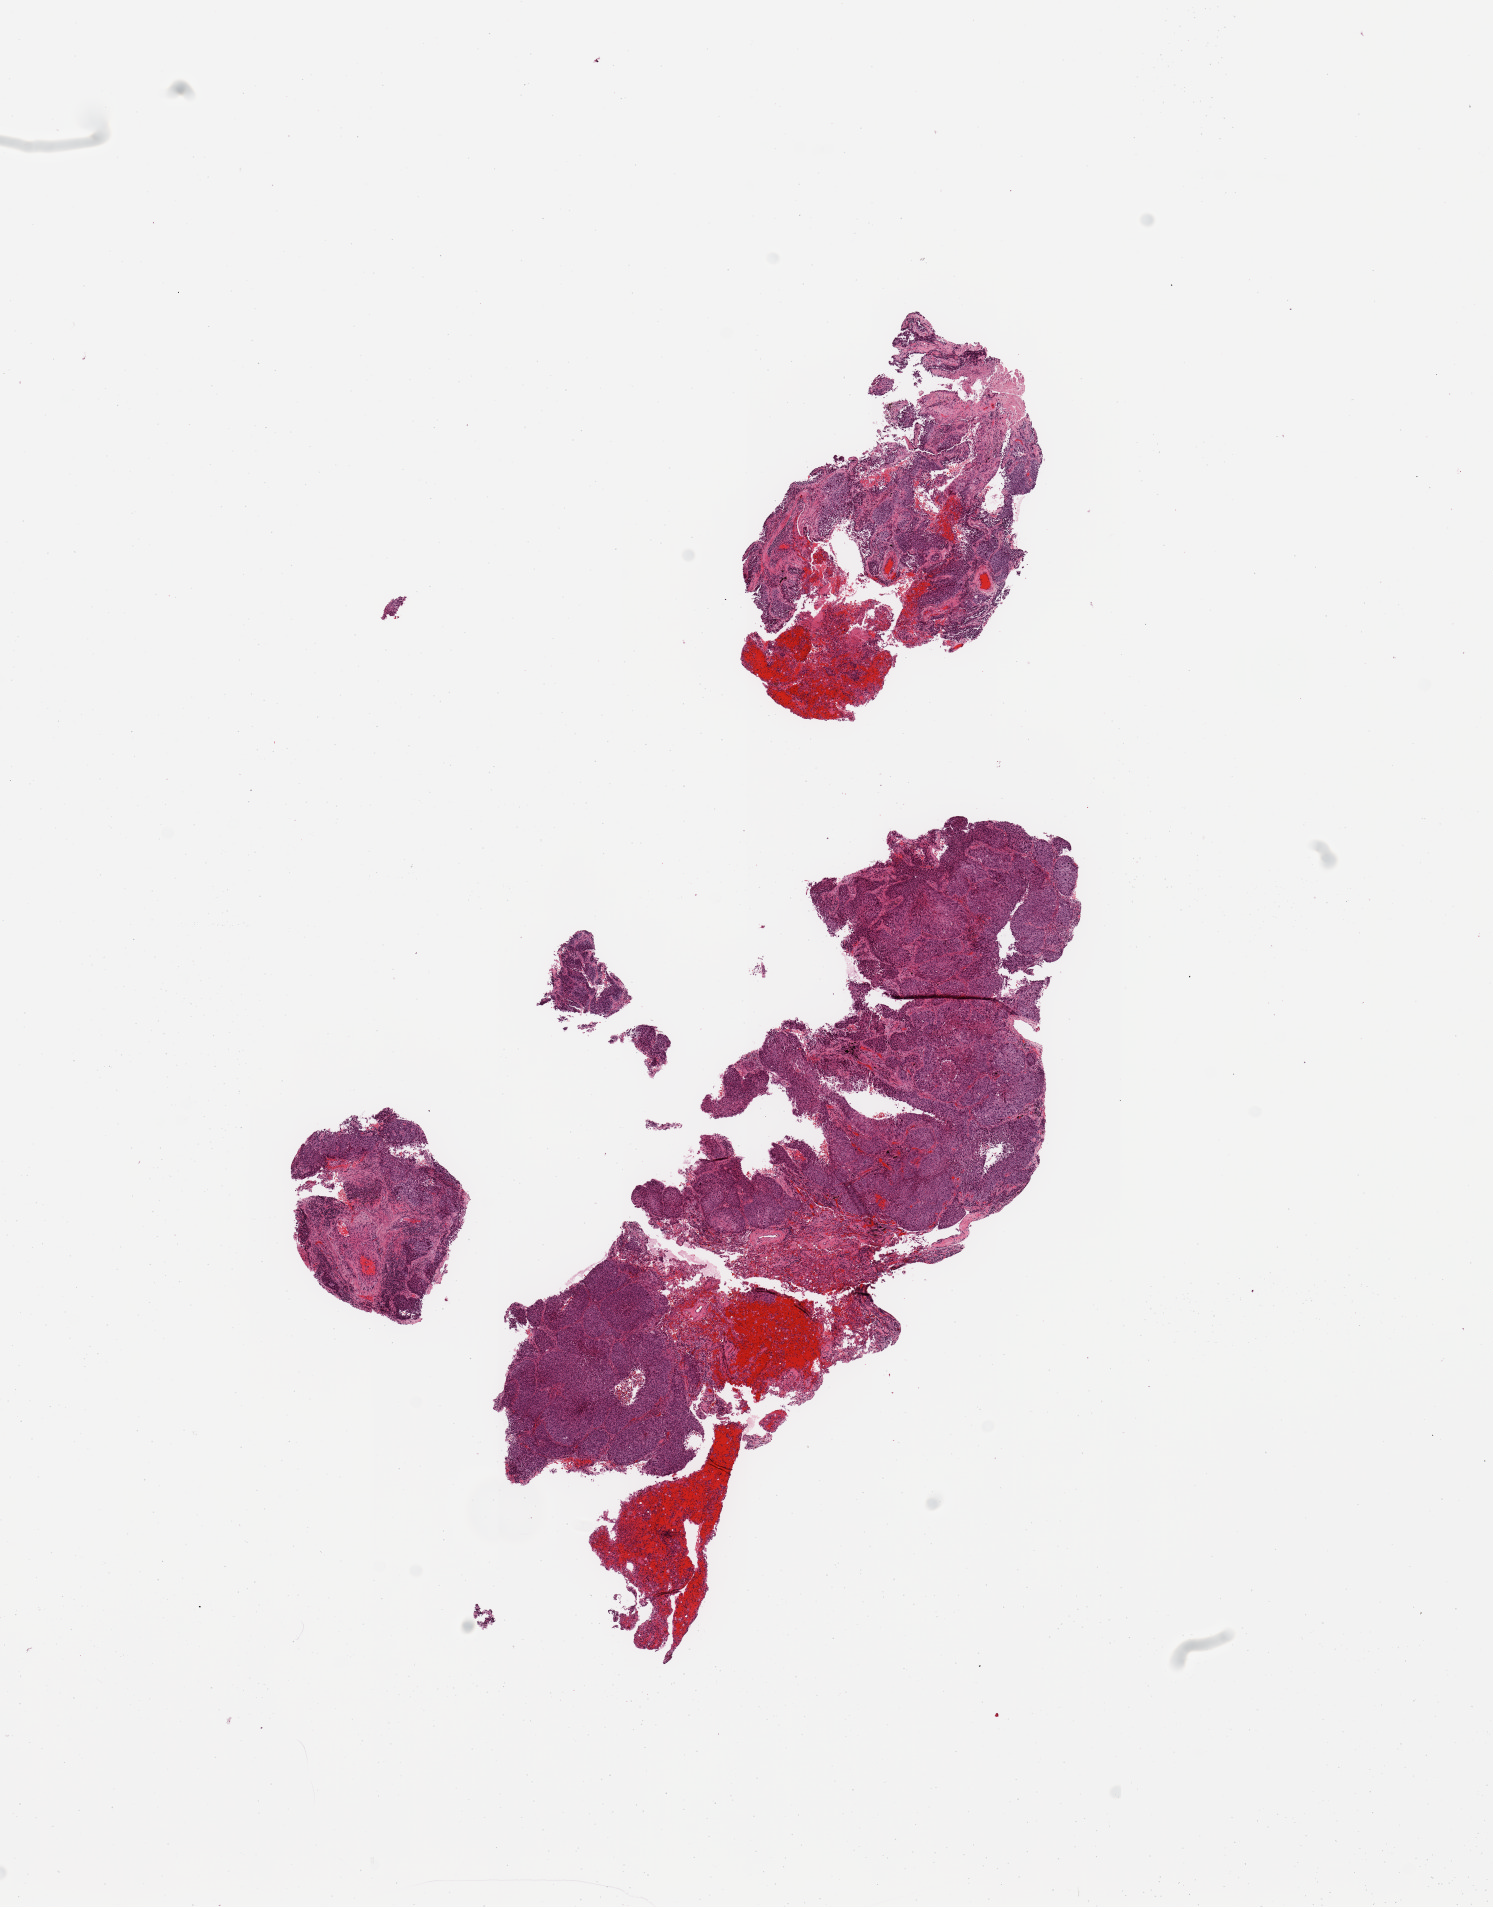
Whole-slide histology image, Hematoxylin and eosin (H&E) stained, shown as a low-resolution overview of the whole scanned area (about 11.8 x 15.1 mm), tumour tissue sample, lung. Patient: male, age 74 years. Histologic grade: G2 (moderately differentiated).
Histologic diagnosis: Squamous cell carcinoma, NOS. AJCC pathologic stage: IA. Primary tumour site (as recorded): right upper lobe.